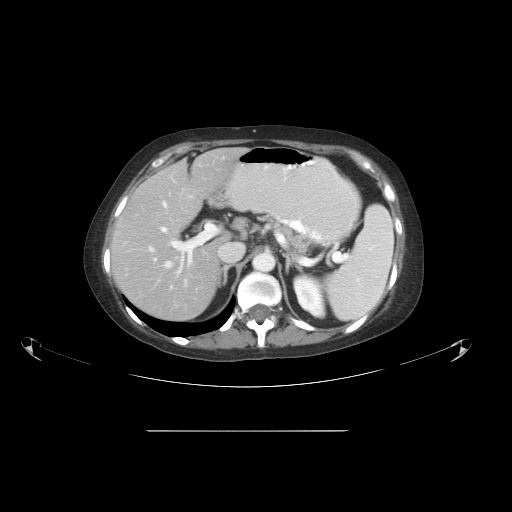
Contrast-enhanced abdominal CT, one axial slice; slice 34 of 51 in the series (ordered by position); reconstruction kernel STANDARD; 120 kVp; intravenous contrast given; soft-tissue window (W 400 / L 40 HU); 5 mm slice thickness; 512 × 512 image matrix, field of view 475 × 475 mm. Female patient, age 48 years. From the clinical record (not read from this slice): diagnosis: colorectal cancer liver metastases, imaged before liver resection; multiple liver metastases: yes; largest metastasis: 1 cm; disease in both lobes: no.
Annotated regions visible in this slice (manually delineated by an expert):
- hepatic veins: bounding box <145,202,220,286> (left, top, right, bottom; pixels)
- liver: <110,149,244,322>
- planned liver remnant (the part of the liver to remain after resection): <110,161,226,322>
- portal vein (with intrahepatic branches): <153,196,214,288>